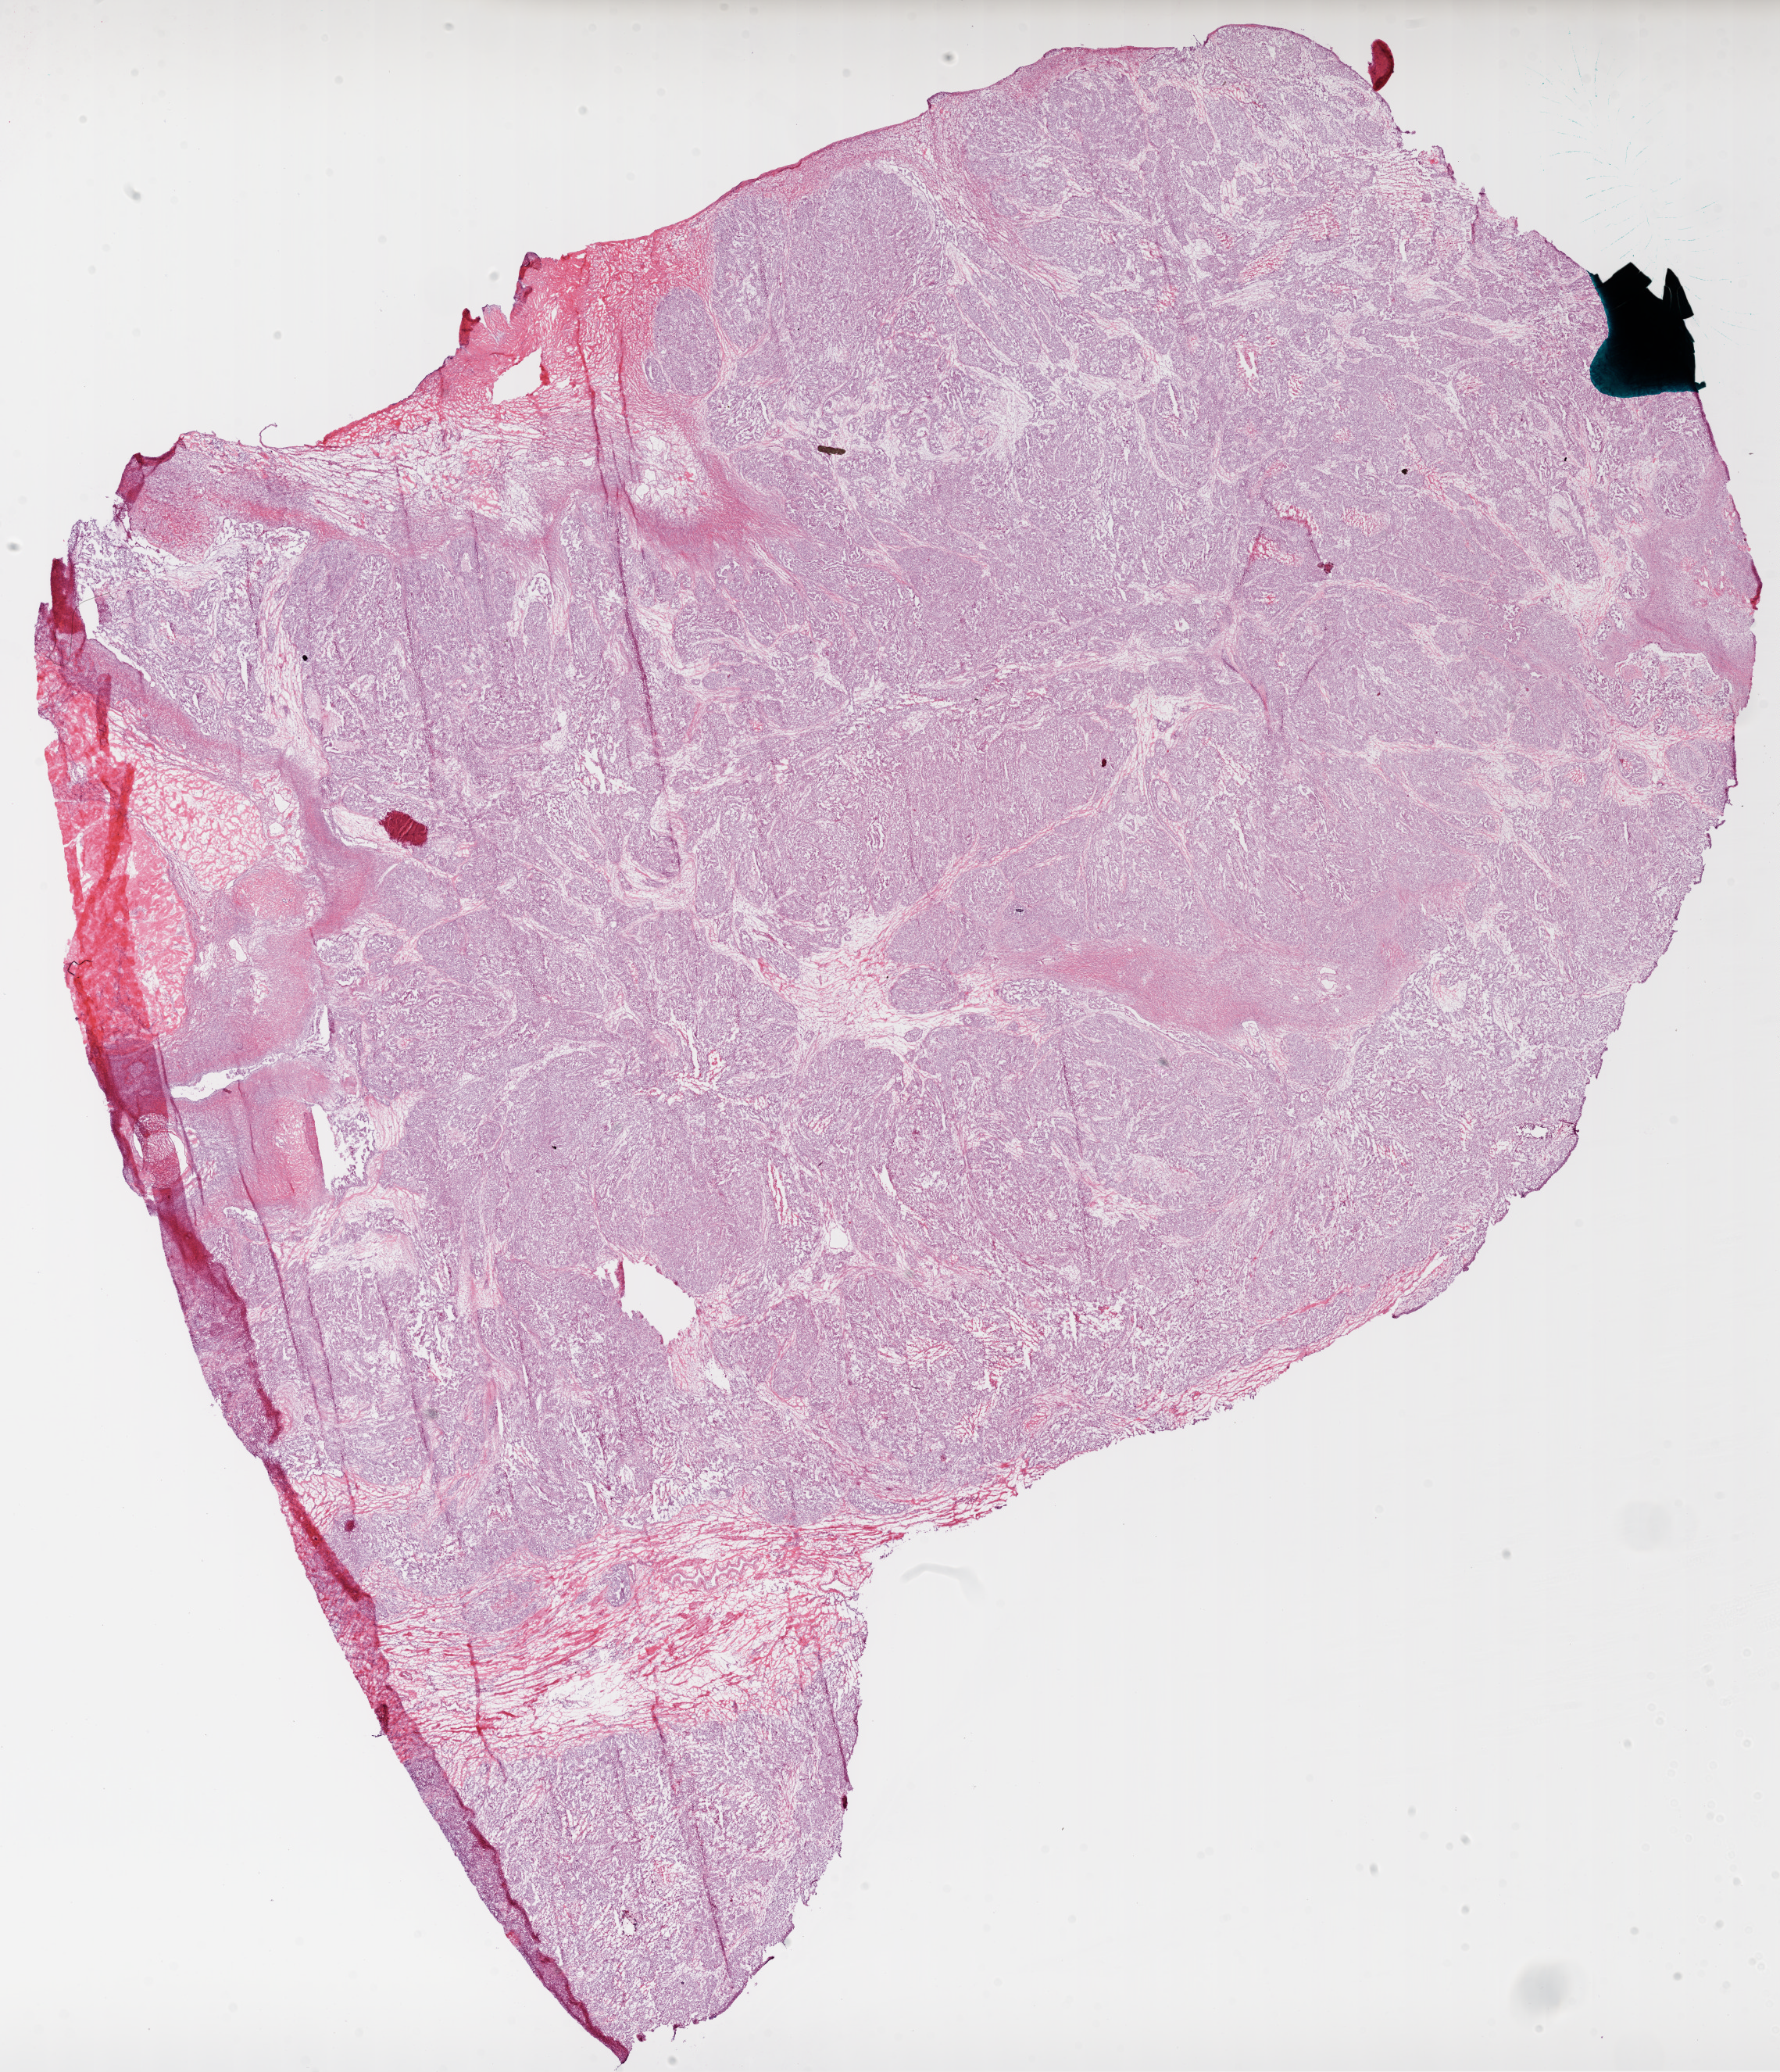
H&E-stained whole-slide image — whole scanned area (about 18.4 x 21.4 mm, from a 20x scan) shown as a low-resolution overview. Frozen section from the bottom of the tissue portion. Sample: primary tumour, ovary. Patient: female, age at initial diagnosis 62 years. Histologic grade: G3 (poorly differentiated). Slide review estimates, as recorded: tumour cells 75%, tumour nuclei 95%, stromal cells 10%, necrosis 15%.
Histologic diagnosis: Serous cystadenocarcinoma, NOS. FIGO stage: IV. Laterality: bilateral.